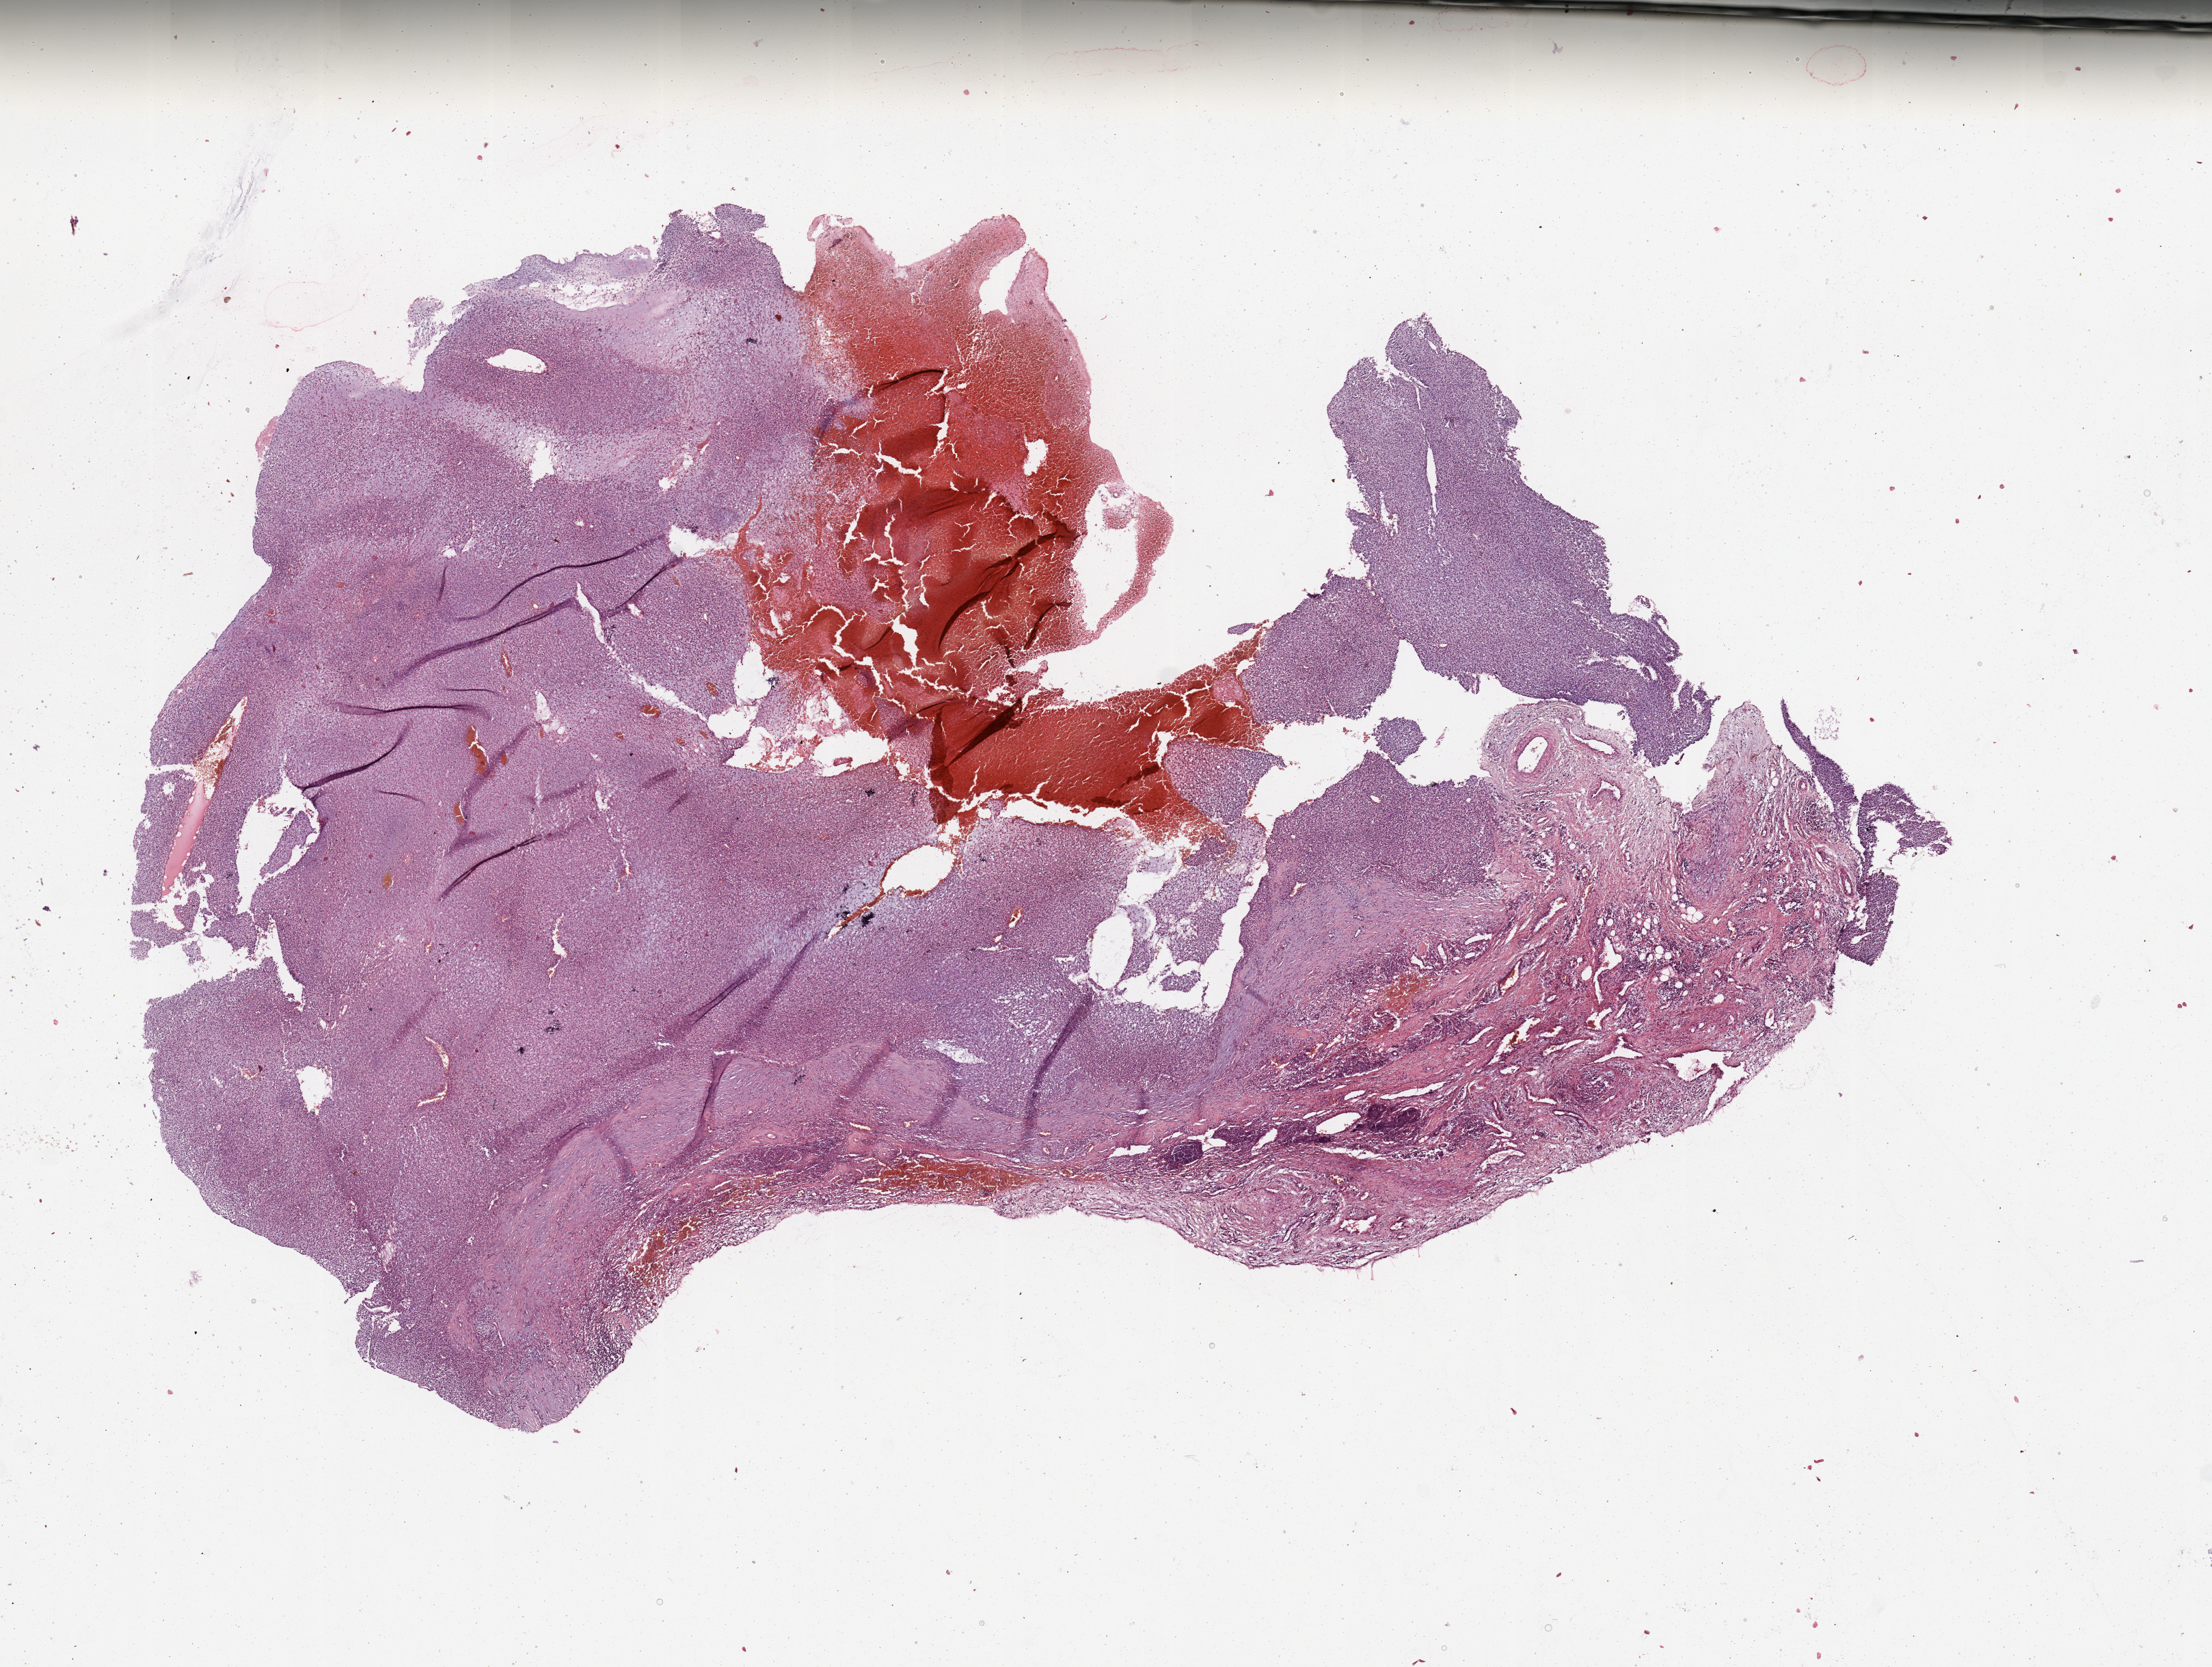
Digitized H&E tissue section (whole slide) — shown as a low-resolution overview of the whole scanned area (about 12.8 x 9.6 mm, from a 20x scan). Melanoma tumour tissue; sampled site not recorded. Patient: female, age 68 years.
Primary tumour site (as recorded): extremities. AJCC pathologic stage: IB. Diagnosis: Malignant melanoma, NOS.